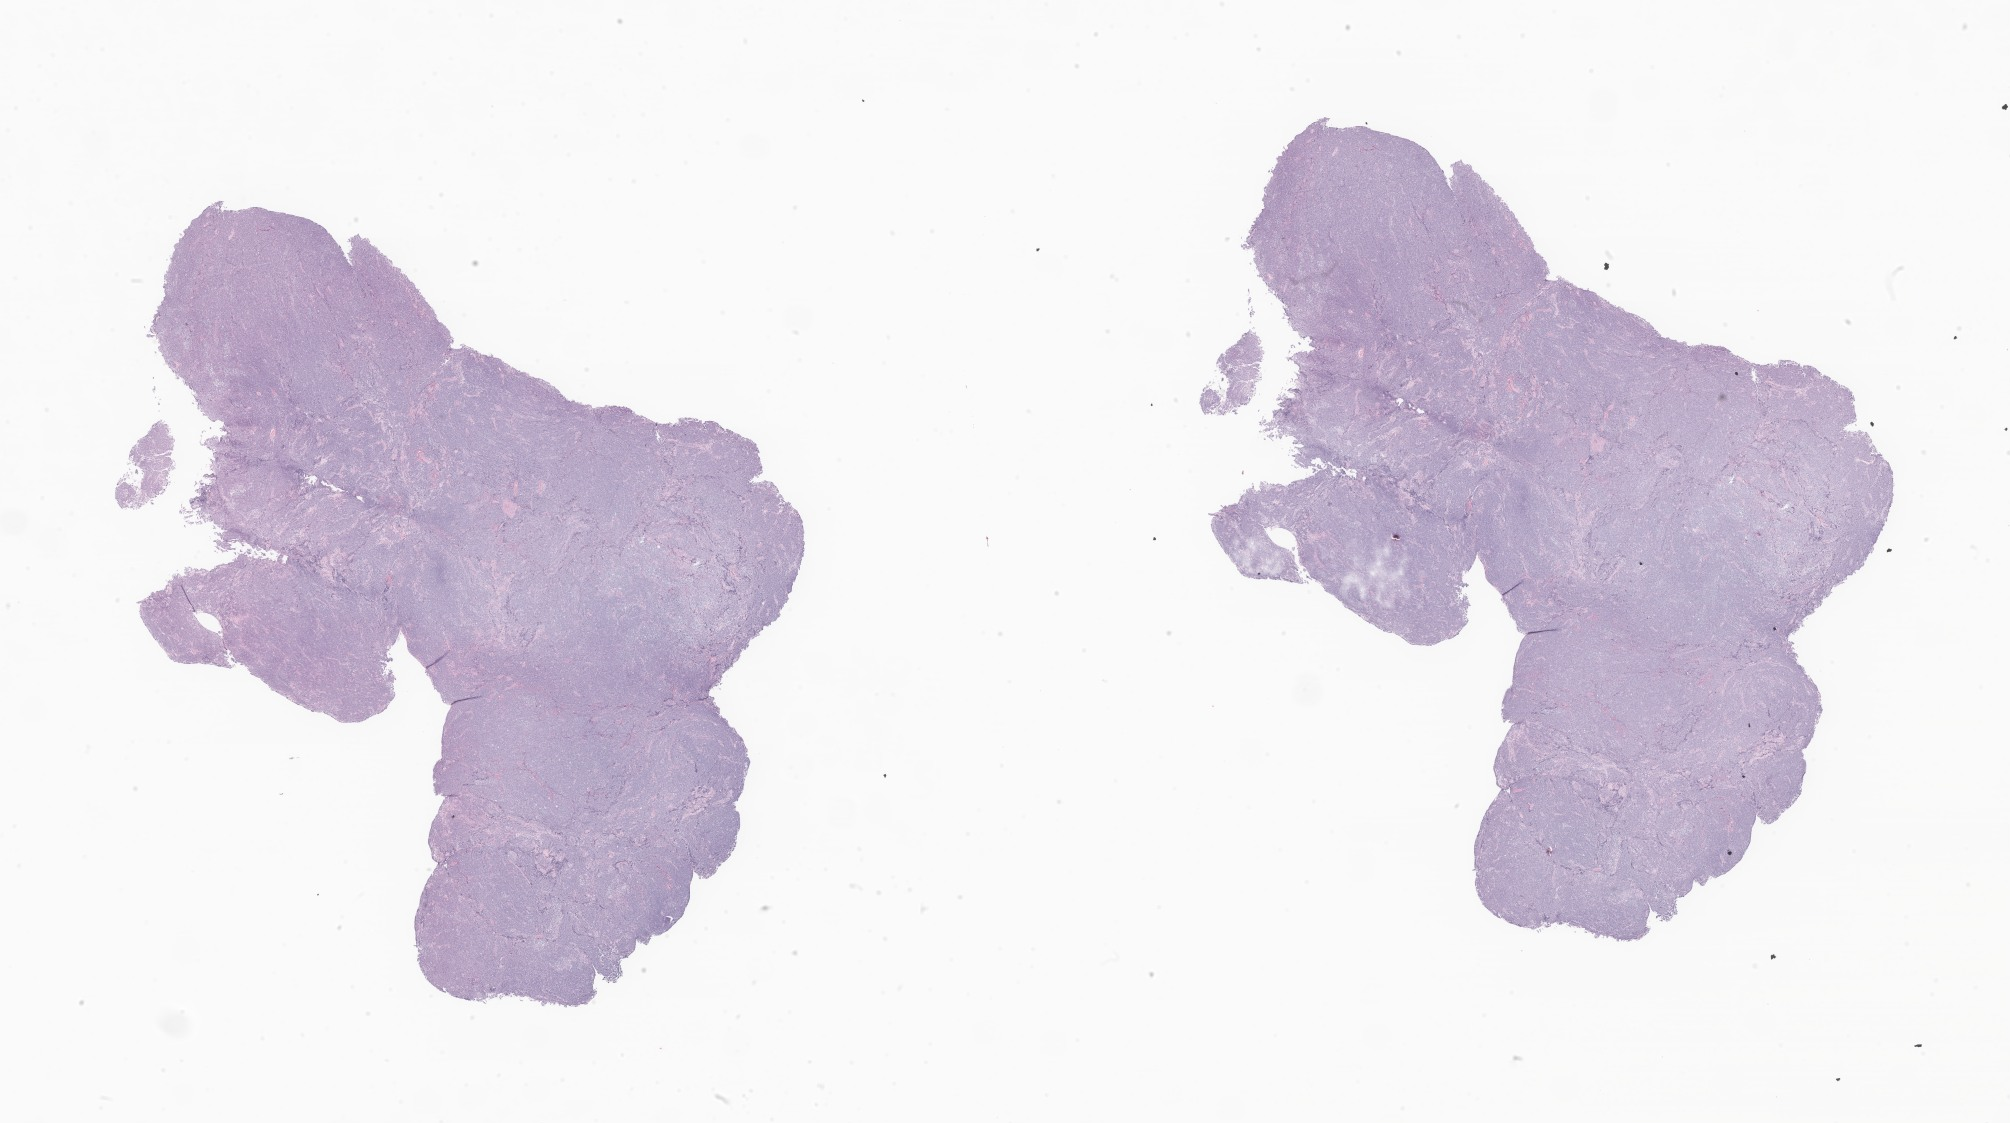
Whole-slide image, hematoxylin and eosin (H&E) stain of tumor tissue from the cerebral ventricle — a low-resolution overview of the entire scanned area, about 33.9 x 18.9 mm; formalin-fixed paraffin-embedded section. Female patient, age 152 months.
Diagnosis: Medulloblastoma, NOS.